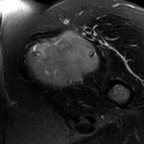
MRI of an extremity soft-tissue mass, one axial slice. Slice 46 of 60 in the series (ordered by position). T2-weighted fat-saturated. MR volume resampled by the dataset authors to the PET/CT grid (not the native acquisition matrix). 3.27 mm slice thickness. 144 × 144 image matrix, field of view 141 × 141 mm. Female patient. From the clinical record (not read from this slice): histological type: pleiomorphic leiomyosarcoma; grade: intermediate; site of the primary tumour: left thigh.
Structures marked on this image (expert contour drawn on MRI and transferred to this co-registered scan by the dataset authors):
- gross tumour volume including surrounding oedema: bounding box [x1, y1, x2, y2] px = [27, 31, 96, 87]
- gross tumour volume (mass): [27, 31, 96, 87]